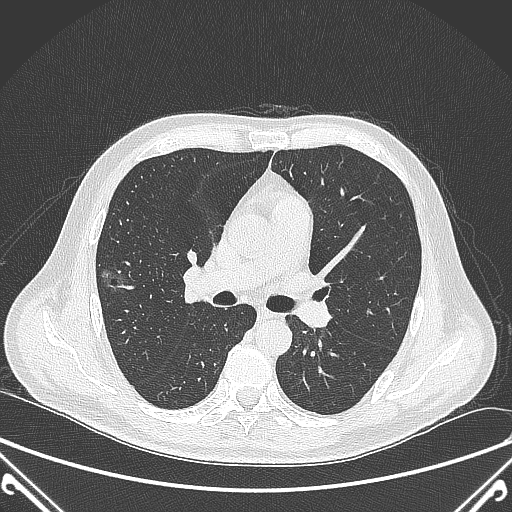
Chest CT, one axial slice; position 220 of 360 along the scan axis; lung window (W 1500 / L -600 HU); 512 × 512 image matrix, field of view 380 × 380 mm. Patient: male, 64 years. From the clinical record (not read from this slice): clinical TNM (as recorded): T1c N0 M0; histopathological grade: G2.
Annotated regions visible in this slice (bounding box drawn by a radiologist):
- lung tumour (recorded histology: adenocarcinoma): box from (x=97, y=268) to (x=144, y=313) px